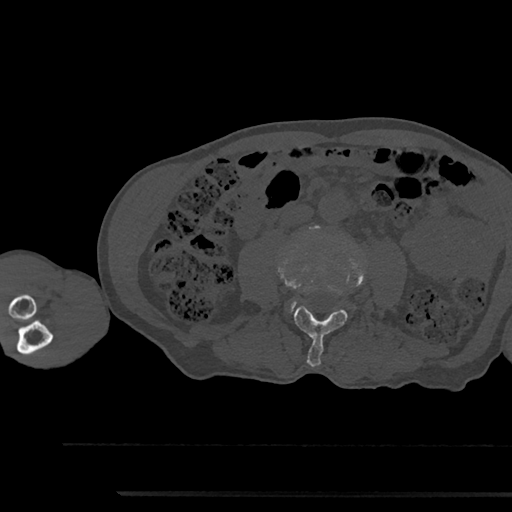
CT including the spine, one axial slice; position 460 of 797 along the scan axis; reconstruction kernel Br40s/3; bone window (W 1800 / L 400 HU); 0.5 mm slice thickness; 512 × 512 image matrix, field of view 367 × 367 mm. Patient: male, 79 years. Case-level facts recorded for this patient, not image findings: primary cancer: prostate.
Structures marked on this image (semi-automatically segmented with operator editing):
- L3 vertebra: box from (x=294, y=257) to (x=365, y=367) px
- L4 vertebra: (x=291, y=301)–(x=296, y=310)